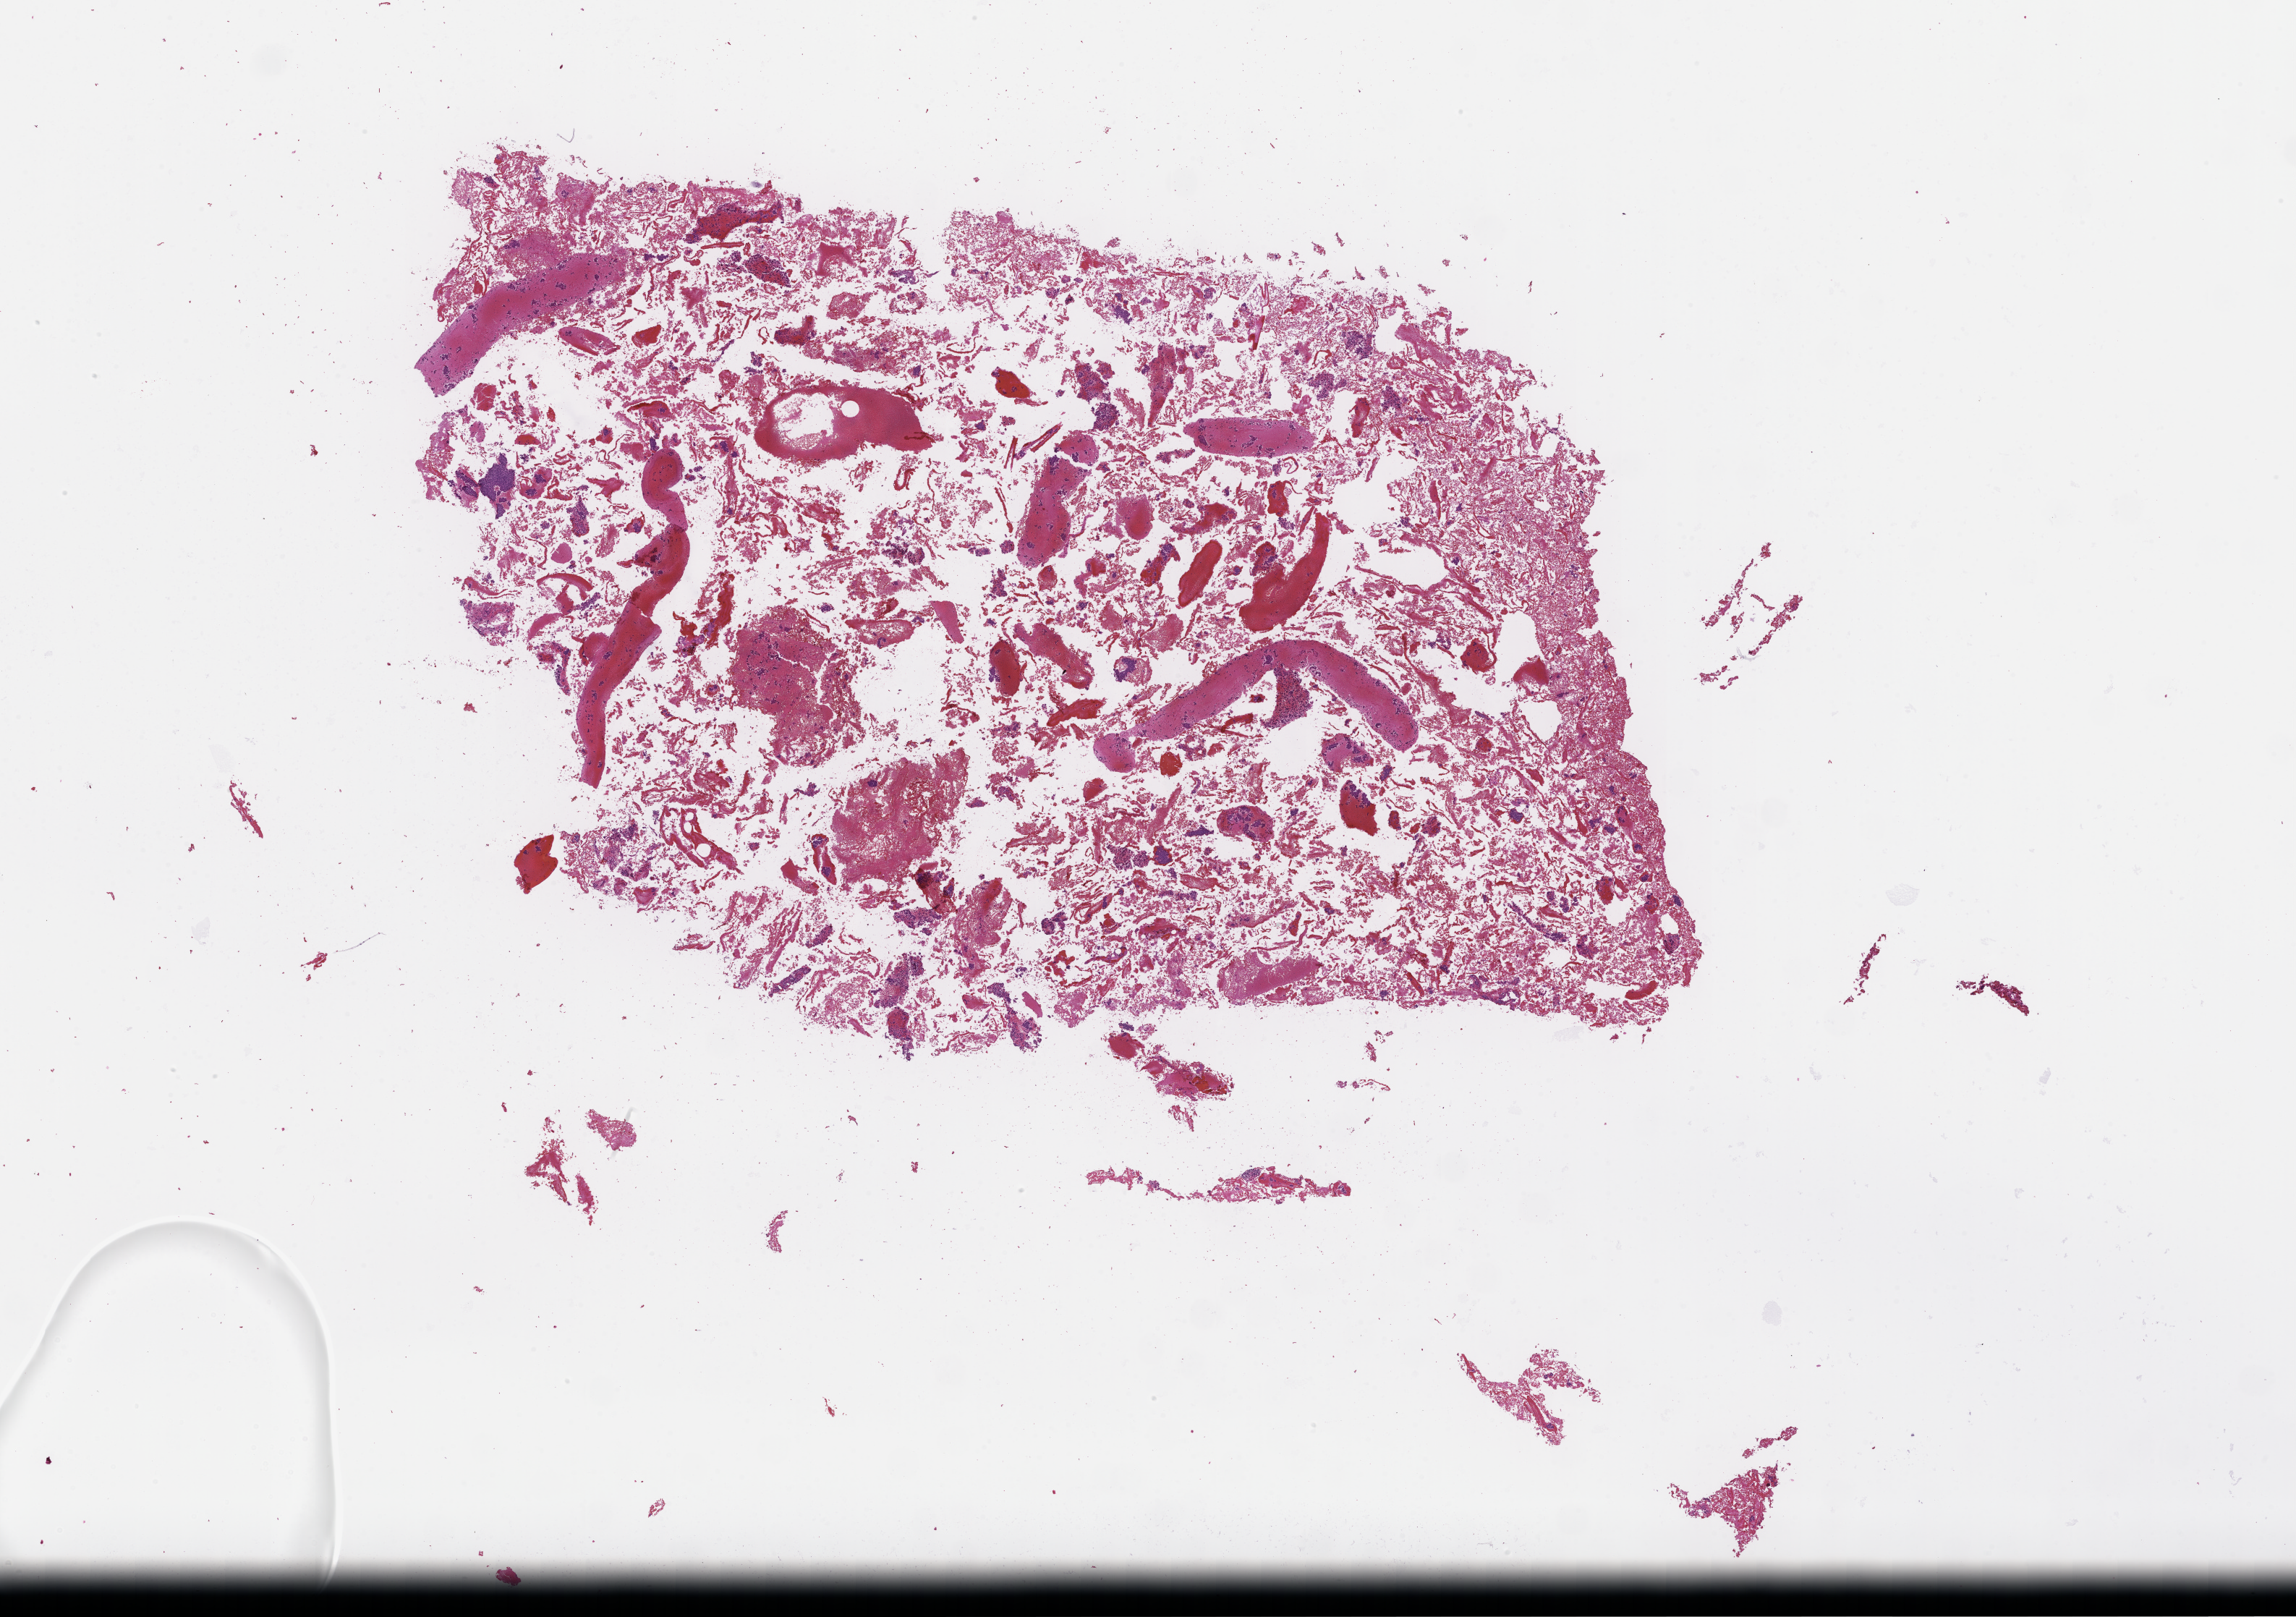
Digitized haematoxylin and eosin-stained section — low-resolution overview of the scanned area, about 25.6 x 18.0 mm. FFPE section. Site: breast. Specimen time point: archival tissue. Patient sex: female.
This section: primary tumor. Diagnosis: Invasive Breast Carcinoma.